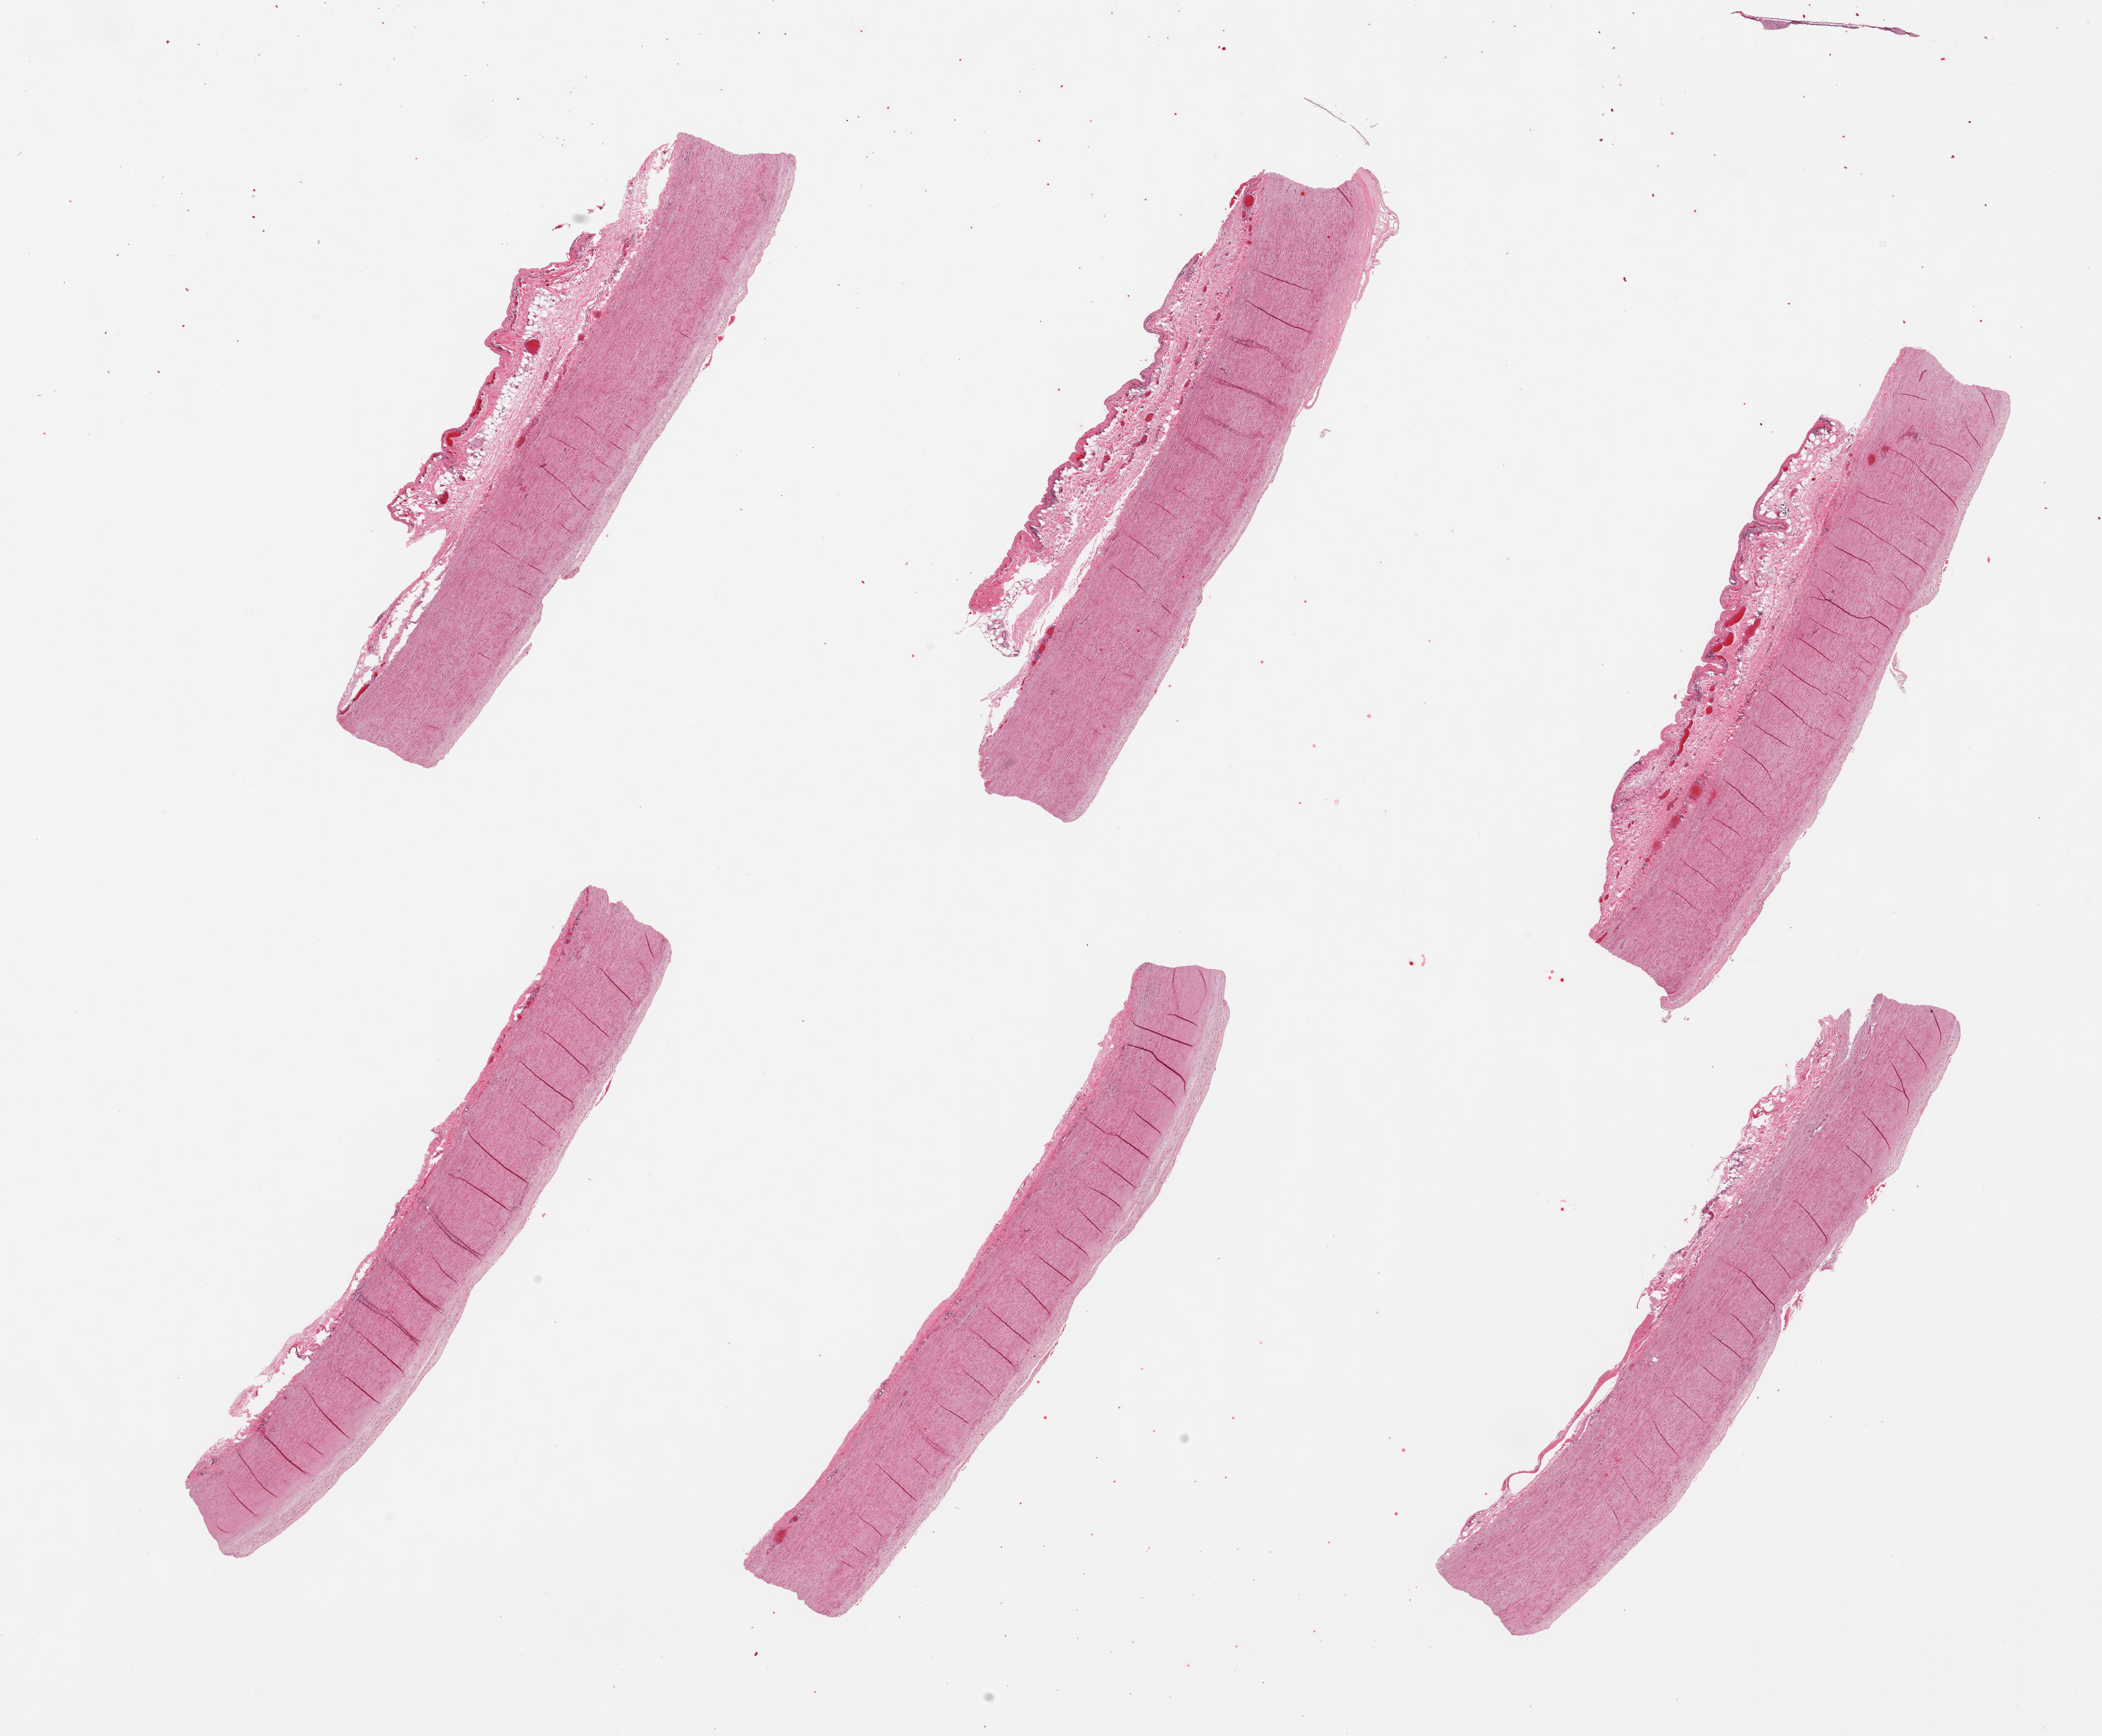
Whole-slide image, haematoxylin and eosin stain — shown as a low-resolution overview of the whole scanned area (about 23.6 x 19.5 mm), PAXgene-fixed paraffin-embedded (PFPE) section, sampled site (target tissue): aorta, donor tissue sample. Female donor.
• reviewer comment on this tissue sample: 6 pieces; flat plaques; thick adventitia [0.7mm] on 3 of 6 pieces